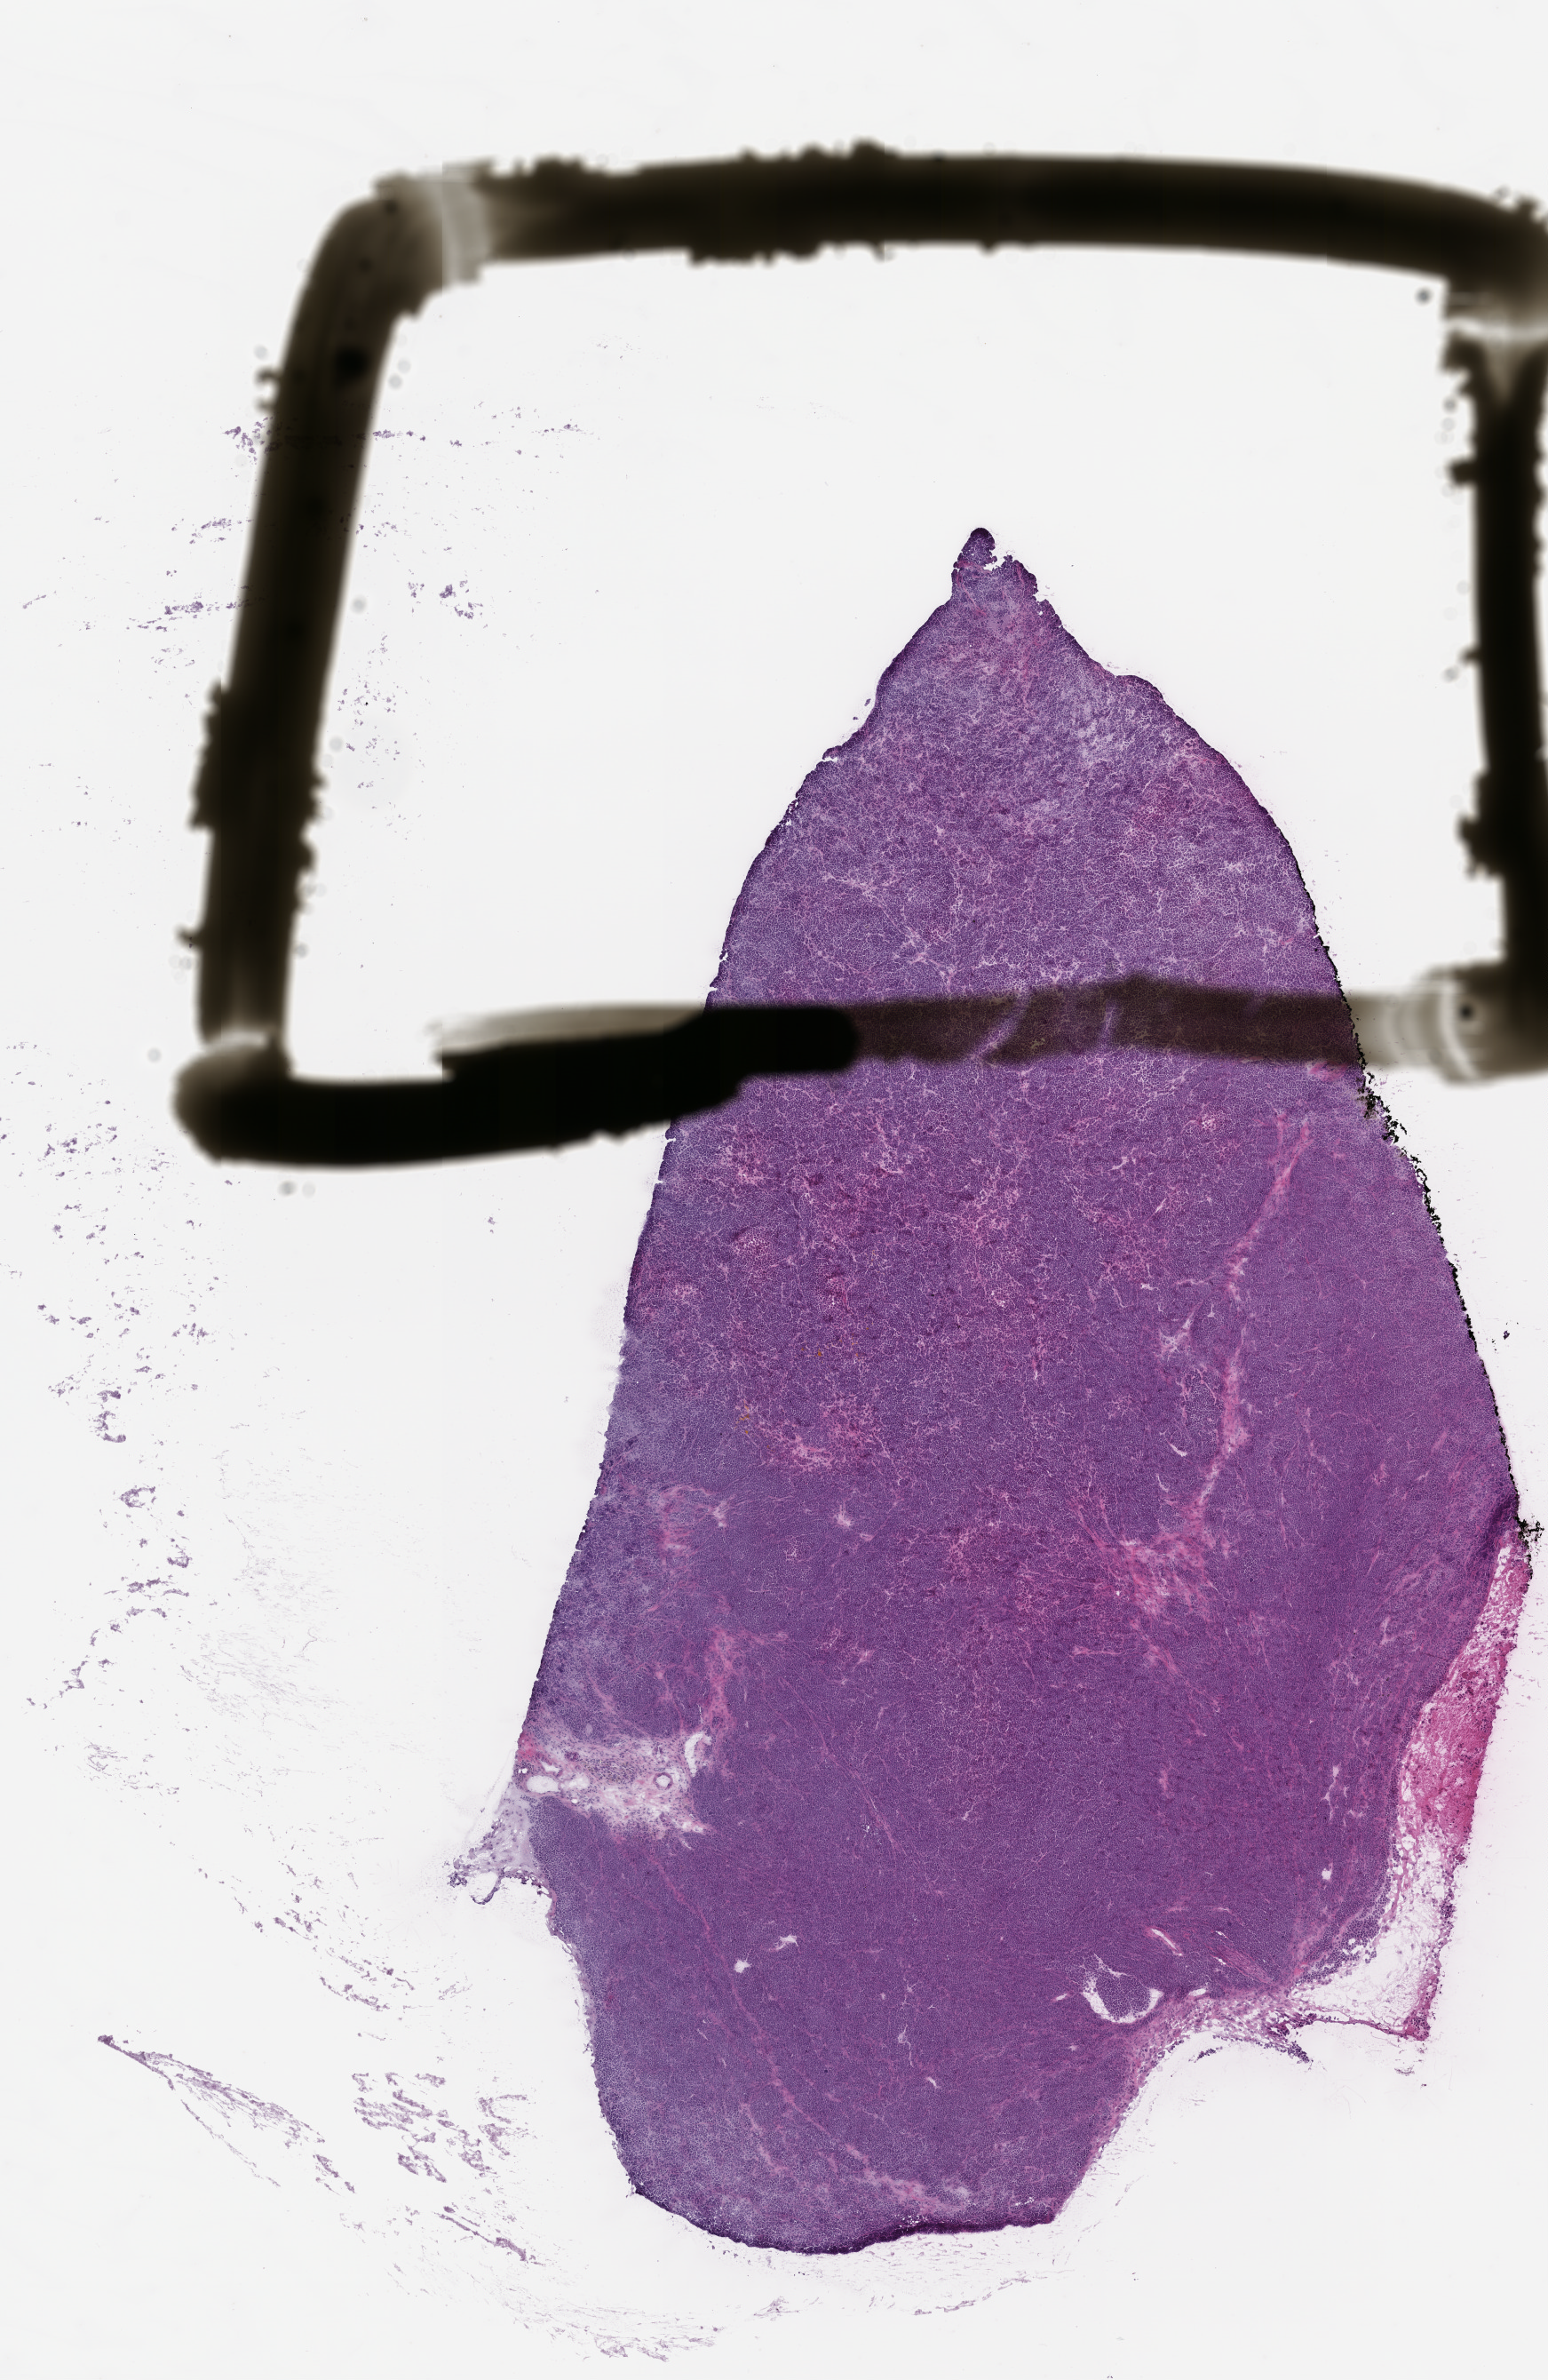
Haematoxylin and eosin whole-slide image of a patient-derived xenograft (PDX) tumor grown in a mouse, passage 0 — low-resolution overview of the scanned area, about 7.0 x 10.8 mm. FFPE section. Originating tumor site category: endocrine.
Originating patient diagnosis: Merkel Cell Carcinoma.